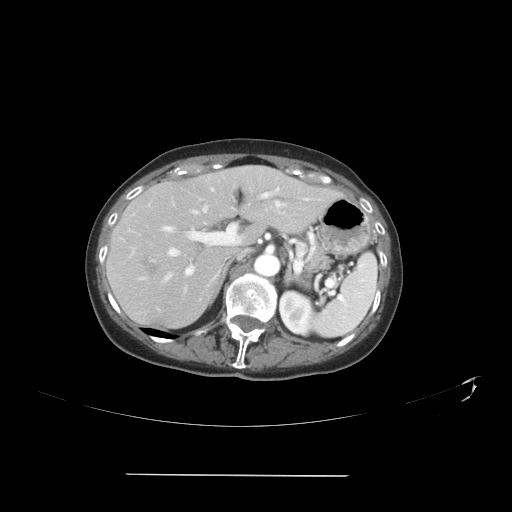
Contrast-enhanced abdominal CT, one axial slice; slice 25 of 41 in the series (ordered by position); 120 kVp; intravenous contrast given; soft-tissue window (W 400 / L 40 HU); 5 mm slice thickness; 512 × 512 image matrix, field of view 431 × 431 mm. Female patient, age 74 years. From the clinical record (not read from this slice): diagnosis: colorectal cancer liver metastases, imaged before liver resection; multiple liver metastases: yes; largest metastasis: 3.3 cm; disease in both lobes: yes.
Outlined on this slice (manually delineated by an expert):
- hepatic veins: box from (x=164, y=201) to (x=280, y=281) px
- liver: (x=108, y=166)–(x=337, y=329)
- planned liver remnant (the part of the liver to remain after resection): (x=117, y=166)–(x=309, y=252)
- portal vein (with intrahepatic branches): (x=163, y=189)–(x=279, y=275)
- liver metastasis: (x=140, y=255)–(x=161, y=278)